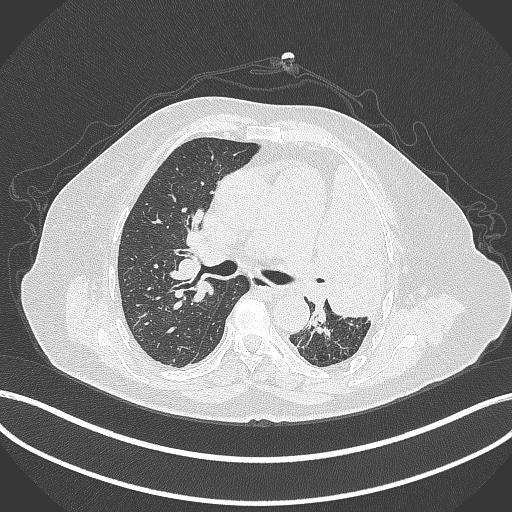
Chest CT, one axial slice. Slice 238 of 399 in the series (ordered by position). 120 kVp. Lung window (W 1500 / L -600 HU). 1 mm slice thickness. 512 × 512 image matrix. Patient: female, 75 years. Case-level facts recorded for this patient, not image findings: clinical TNM (as recorded): T3 N3 M1.
Annotated regions visible in this slice (bounding box drawn by a radiologist):
- lung tumour (recorded histology: adenocarcinoma): bounding box [x1, y1, x2, y2] px = [311, 161, 394, 322]